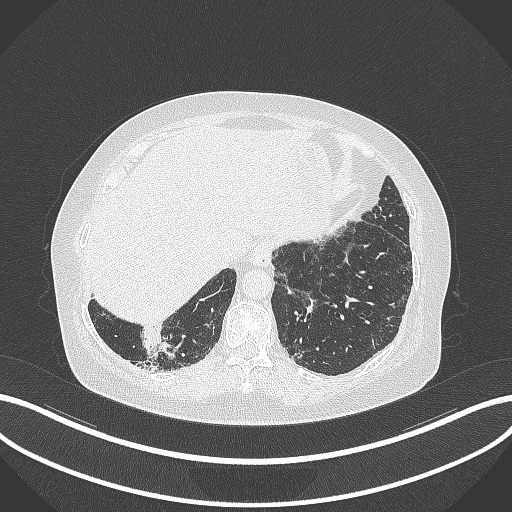
Chest CT, one axial slice; position 20 of 296 along the scan axis; reconstruction kernel B70f; 120 kVp; lung window (W 1500 / L -600 HU); 512 × 512 image matrix, field of view 400 × 400 mm. Patient: female, 65 years. From the clinical record (not read from this slice): clinical TNM (as recorded): T2b N1 M0; histopathological grade: G1.
Structures marked on this image (rectangle marked by the reading radiologist):
- lung tumour (recorded histology: adenocarcinoma): bounding box <136,326,177,364> (left, top, right, bottom; pixels)